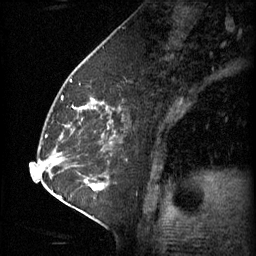
Breast MRI (dynamic contrast-enhanced), one sagittal slice. Position 32 of 60 along the scan axis. 3 images stored at this slice position (order not interpretable as contrast timing). 1.5 T. TE 4.2 ms, TR 11 ms. 2 mm slice thickness. 256 × 256 image matrix, field of view 180 × 180 mm. Patient: female, 62 years.
Structures marked on this image (semi-automatically segmented with operator editing):
- analysis volume of interest (the breast-tissue region the enhancement analysis was run in; not a lesion): bounding box [x1, y1, x2, y2] px = [55, 72, 116, 135]
- tumour enhancement mask (voxels above the 70 % enhancement threshold inside the analysis volume of interest): [86, 98, 94, 109]